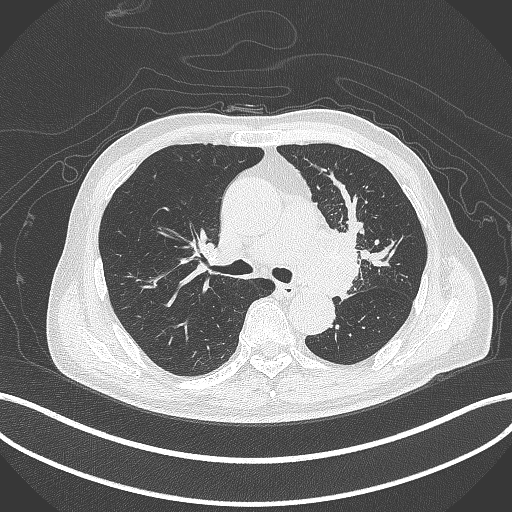
Chest CT, one axial slice. Slice 271 of 417 in the series (ordered by position). Reconstruction kernel B70f. Lung window (W 1500 / L -600 HU). 1 mm slice thickness. 512 × 512 image matrix, field of view 400 × 400 mm. Patient: male, 77 years. Case-level facts recorded for this patient, not image findings: clinical TNM (as recorded): T3 N1 M0.
Outlined on this slice (rectangle marked by the reading radiologist):
- lung tumour (recorded histology: adenocarcinoma): box from (x=312, y=224) to (x=369, y=304) px